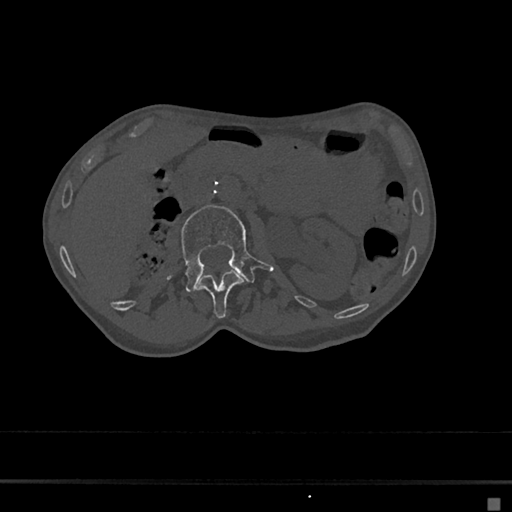
CT including the spine, one axial slice. Slice 33 of 797 in the series (ordered by position). Bone window (W 1800 / L 400 HU). 0.5 mm slice thickness. 512 × 512 image matrix, field of view 360 × 360 mm. Female patient, age 68 years. From the clinical record (not read from this slice): primary cancer: renal.
Annotated regions visible in this slice (semi-automatic segmentation, software-assisted and operator-edited):
- L1 vertebra: box from (x=196, y=270) to (x=244, y=319) px
- L2 vertebra: (x=181, y=205)–(x=273, y=291)